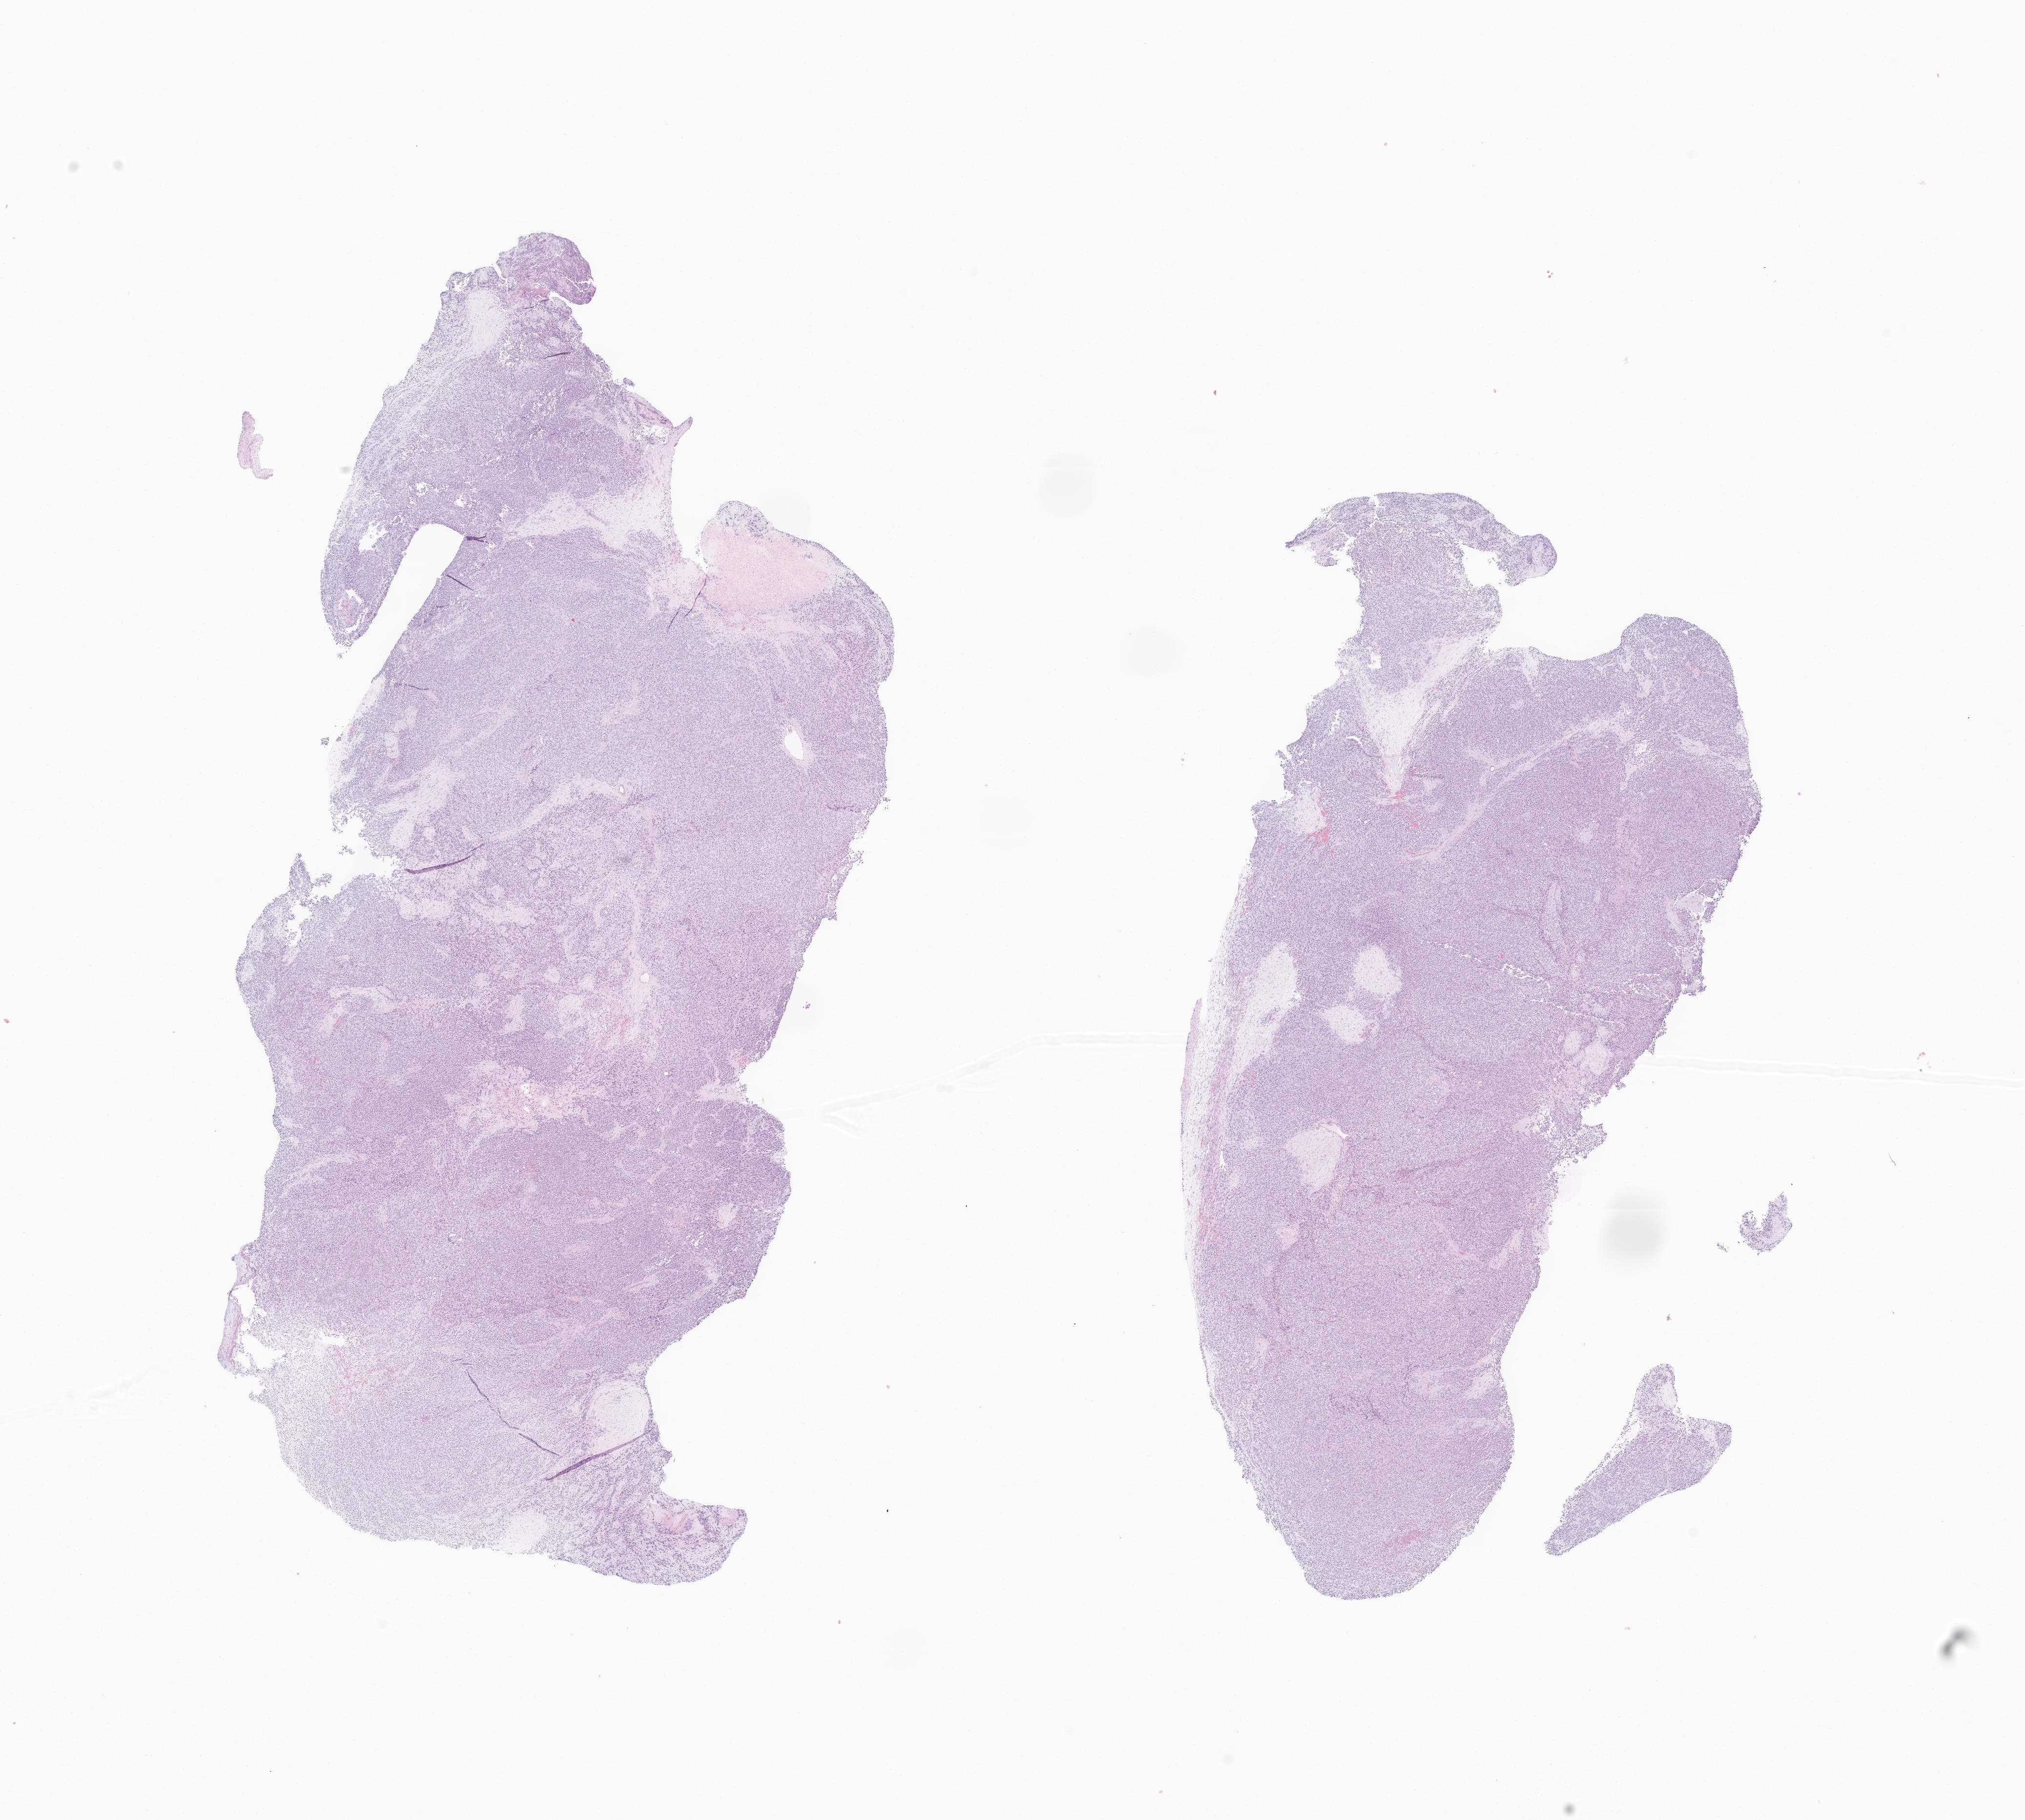
Hematoxylin and eosin (H&E) whole-slide image of tumor tissue from the liver — a low-resolution overview of the entire scanned area, about 17.5 x 15.7 mm; formalin-fixed, paraffin-embedded (FFPE) tissue. Patient: female, age 219 months (18 years 3 months).
- diagnosis: Adrenal cortical carcinoma